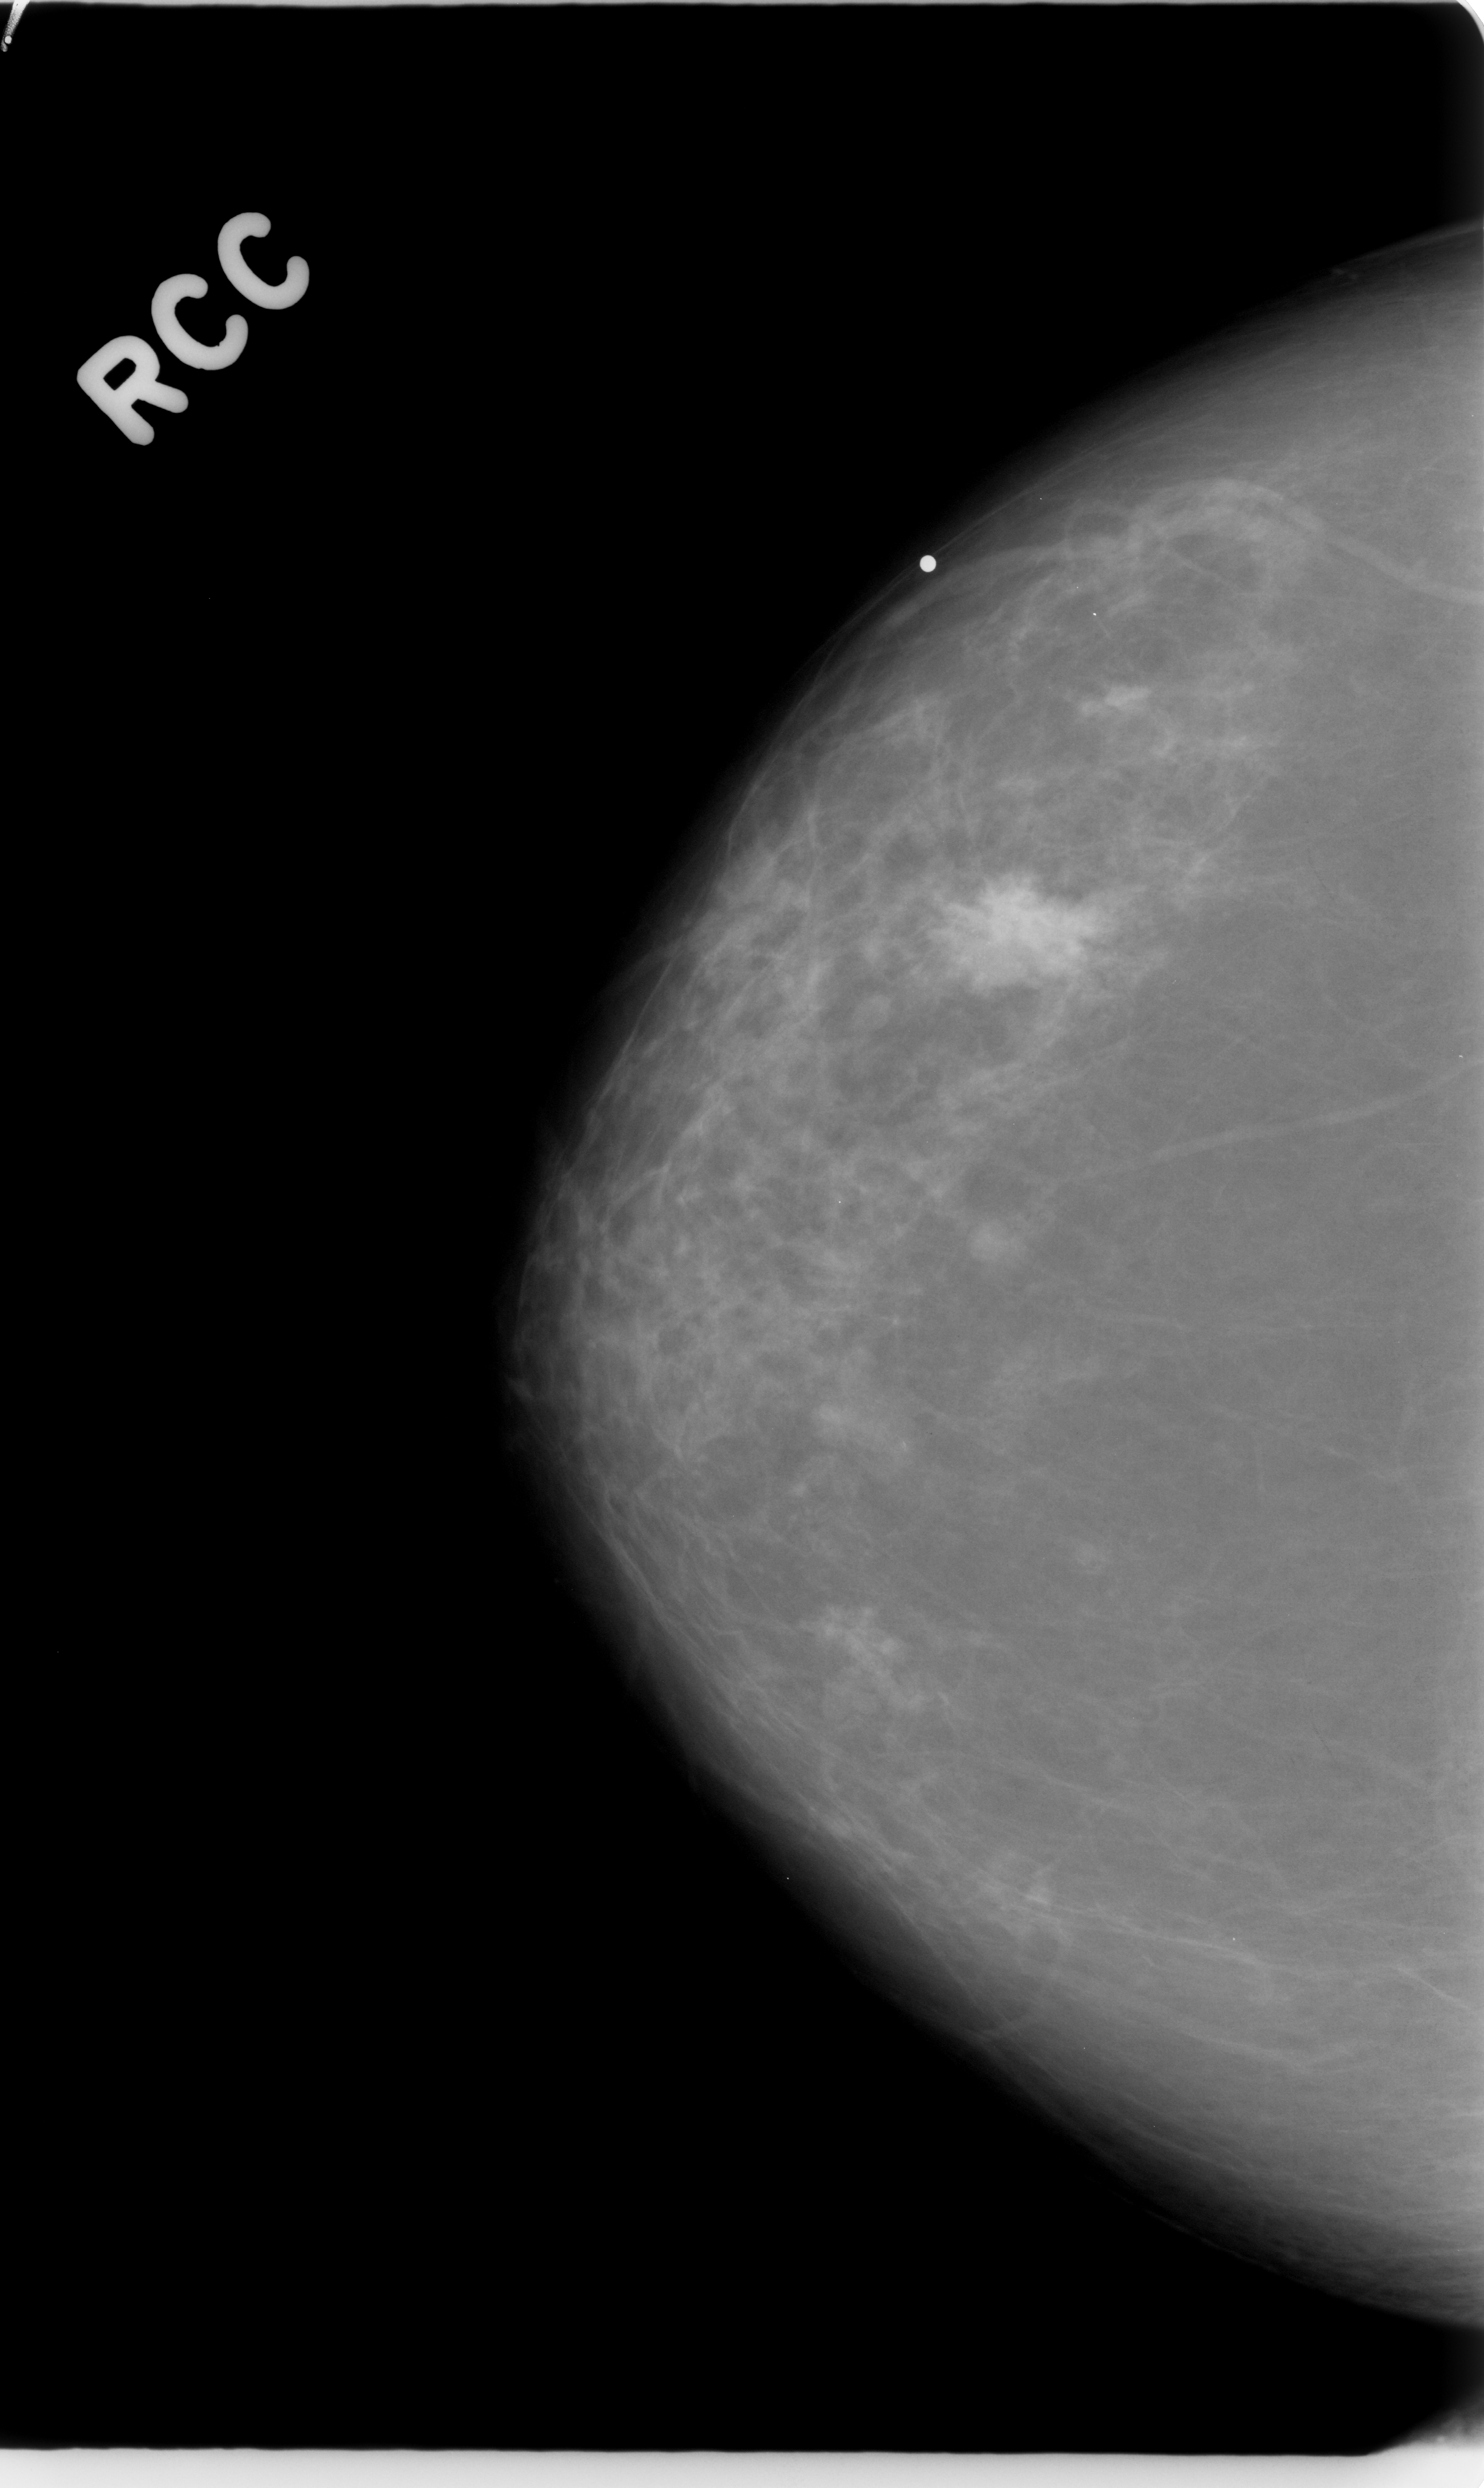
Scanned film-screen mammogram; right breast; CC view; breast composition: almost entirely fatty (BI-RADS density category 1 of 4).
Marked abnormality: mass, shape irregular, margins spiculated; BI-RADS assessment category 5; pathology result (as recorded, not read from the image): malignant.